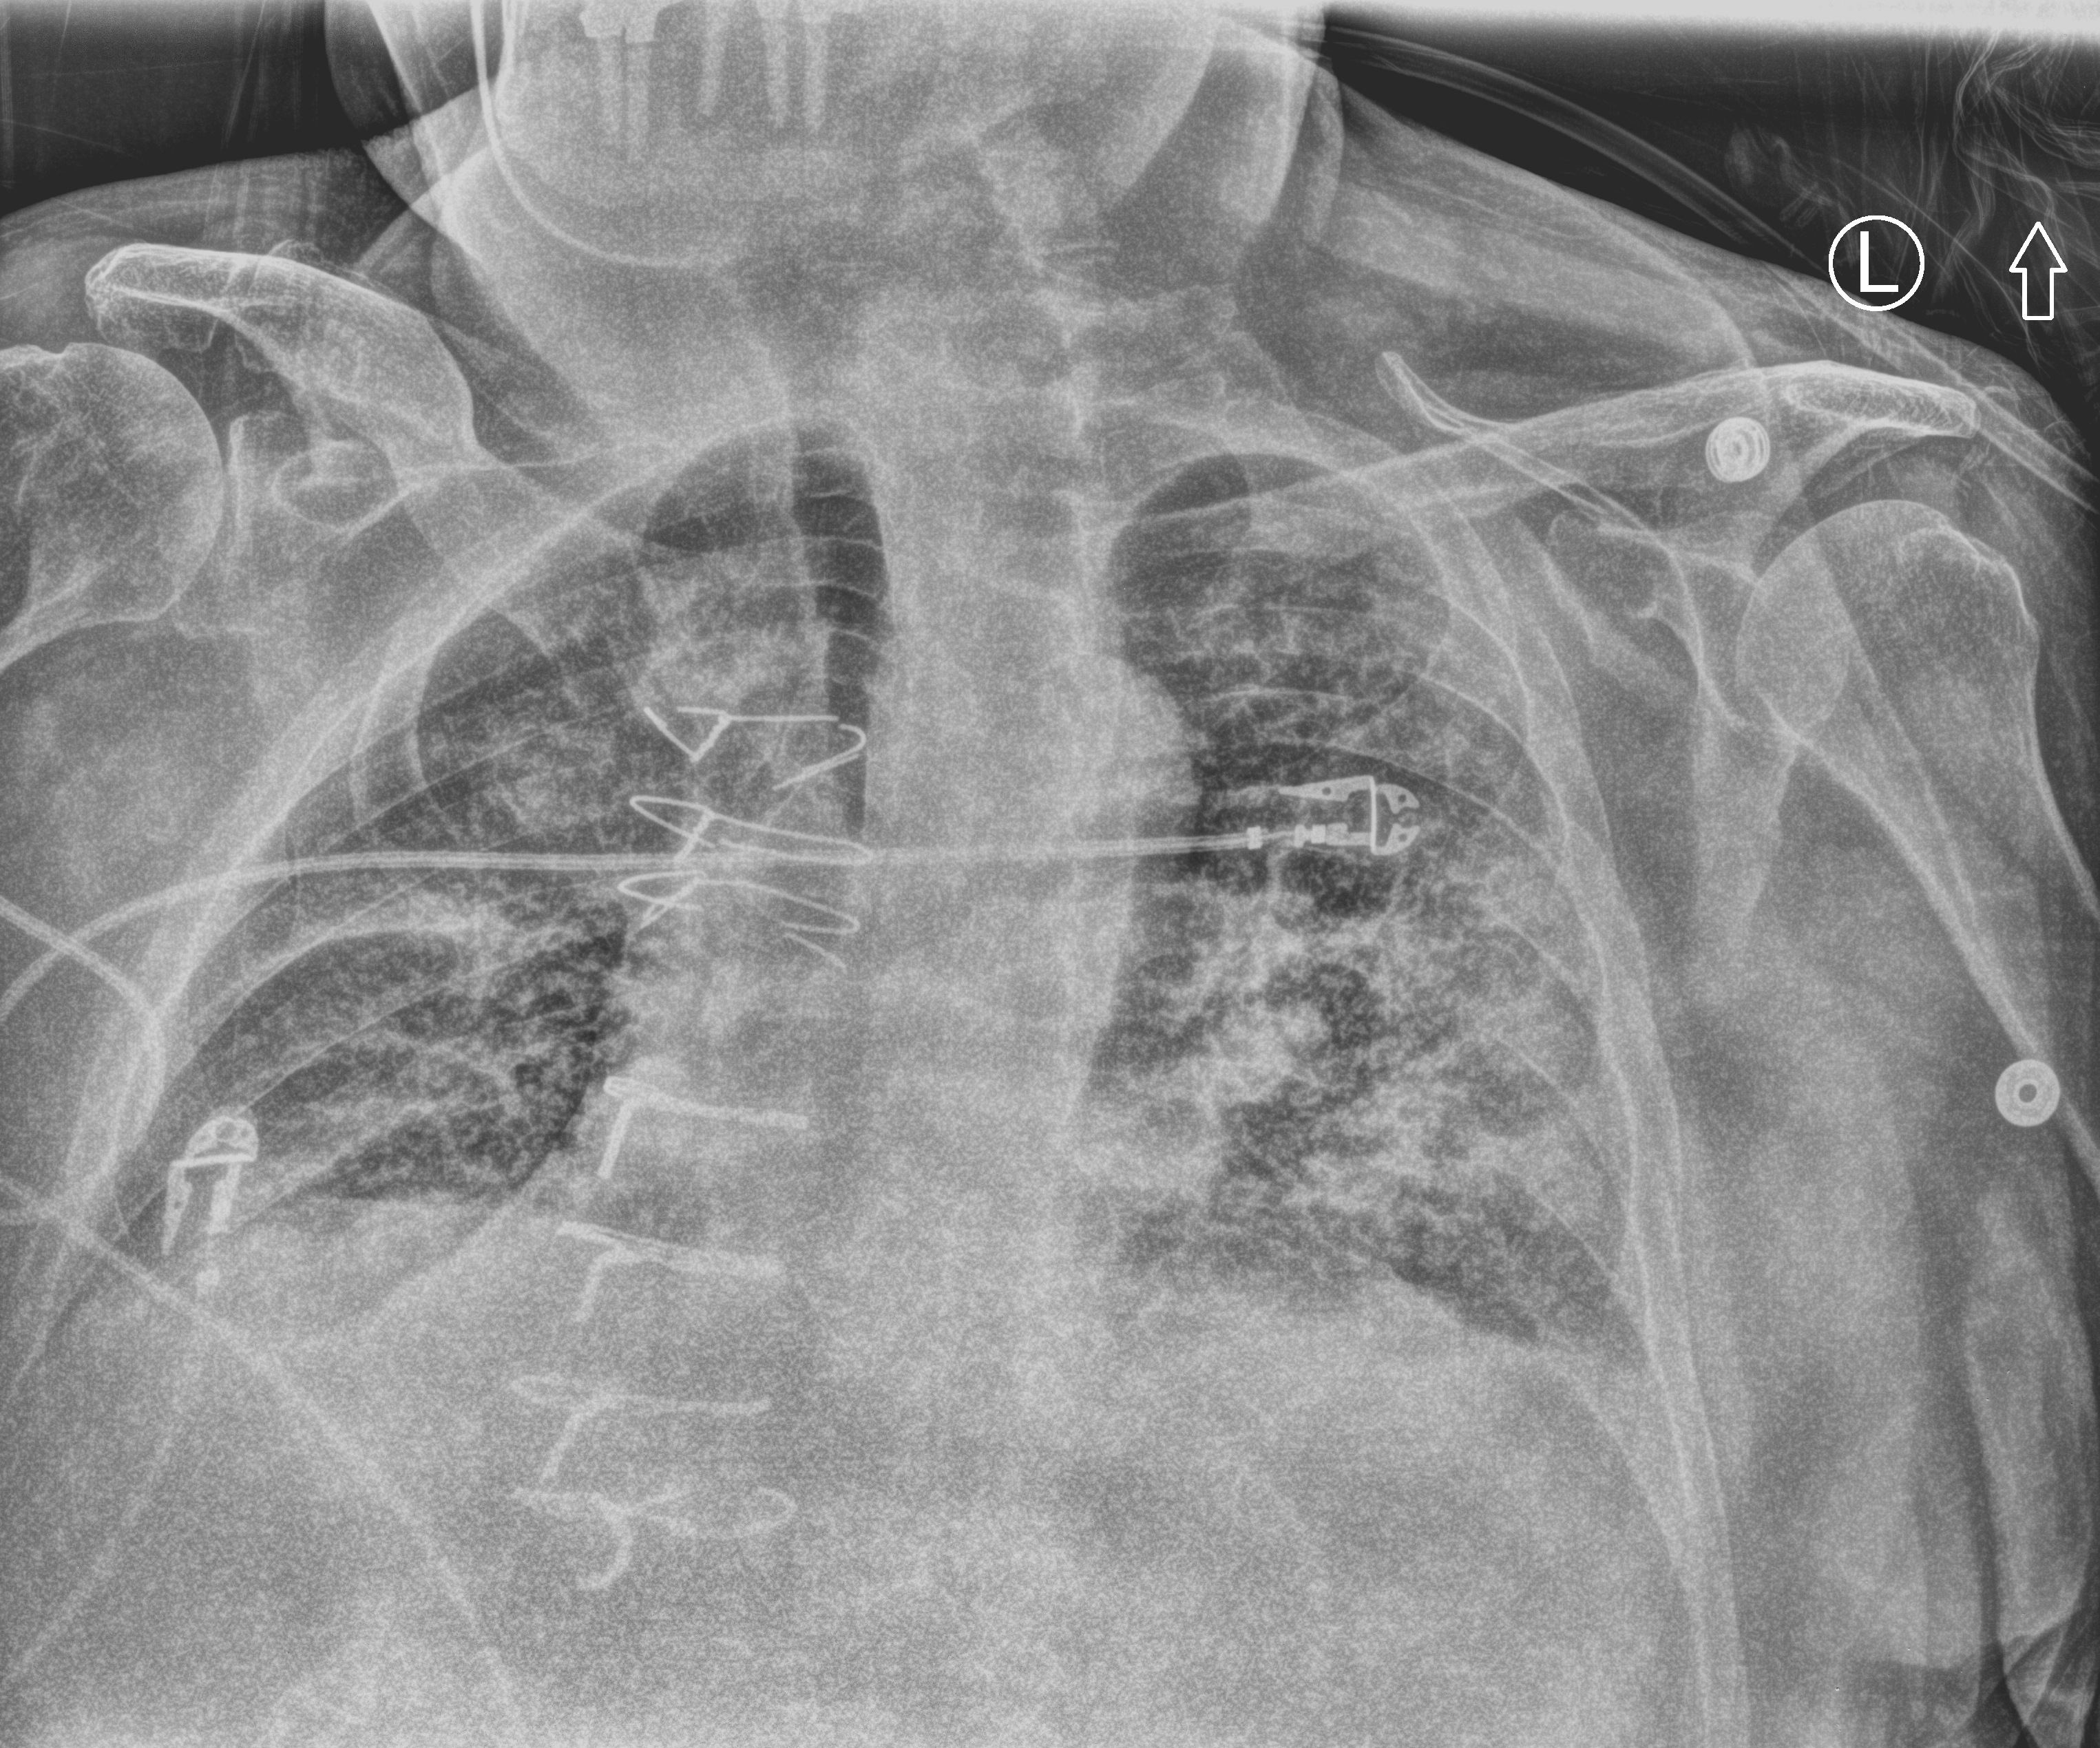
Portable chest radiograph; anteroposterior (AP) projection. Male patient hospitalised with COVID-19, age 75–90 years.
Hospital-stay facts (about this admission, not read from this image; timing relative to this image not recorded):
- mechanically ventilated during this hospital stay: no
- other chronic lung disease (admission record): yes
- diabetes (admission record): yes